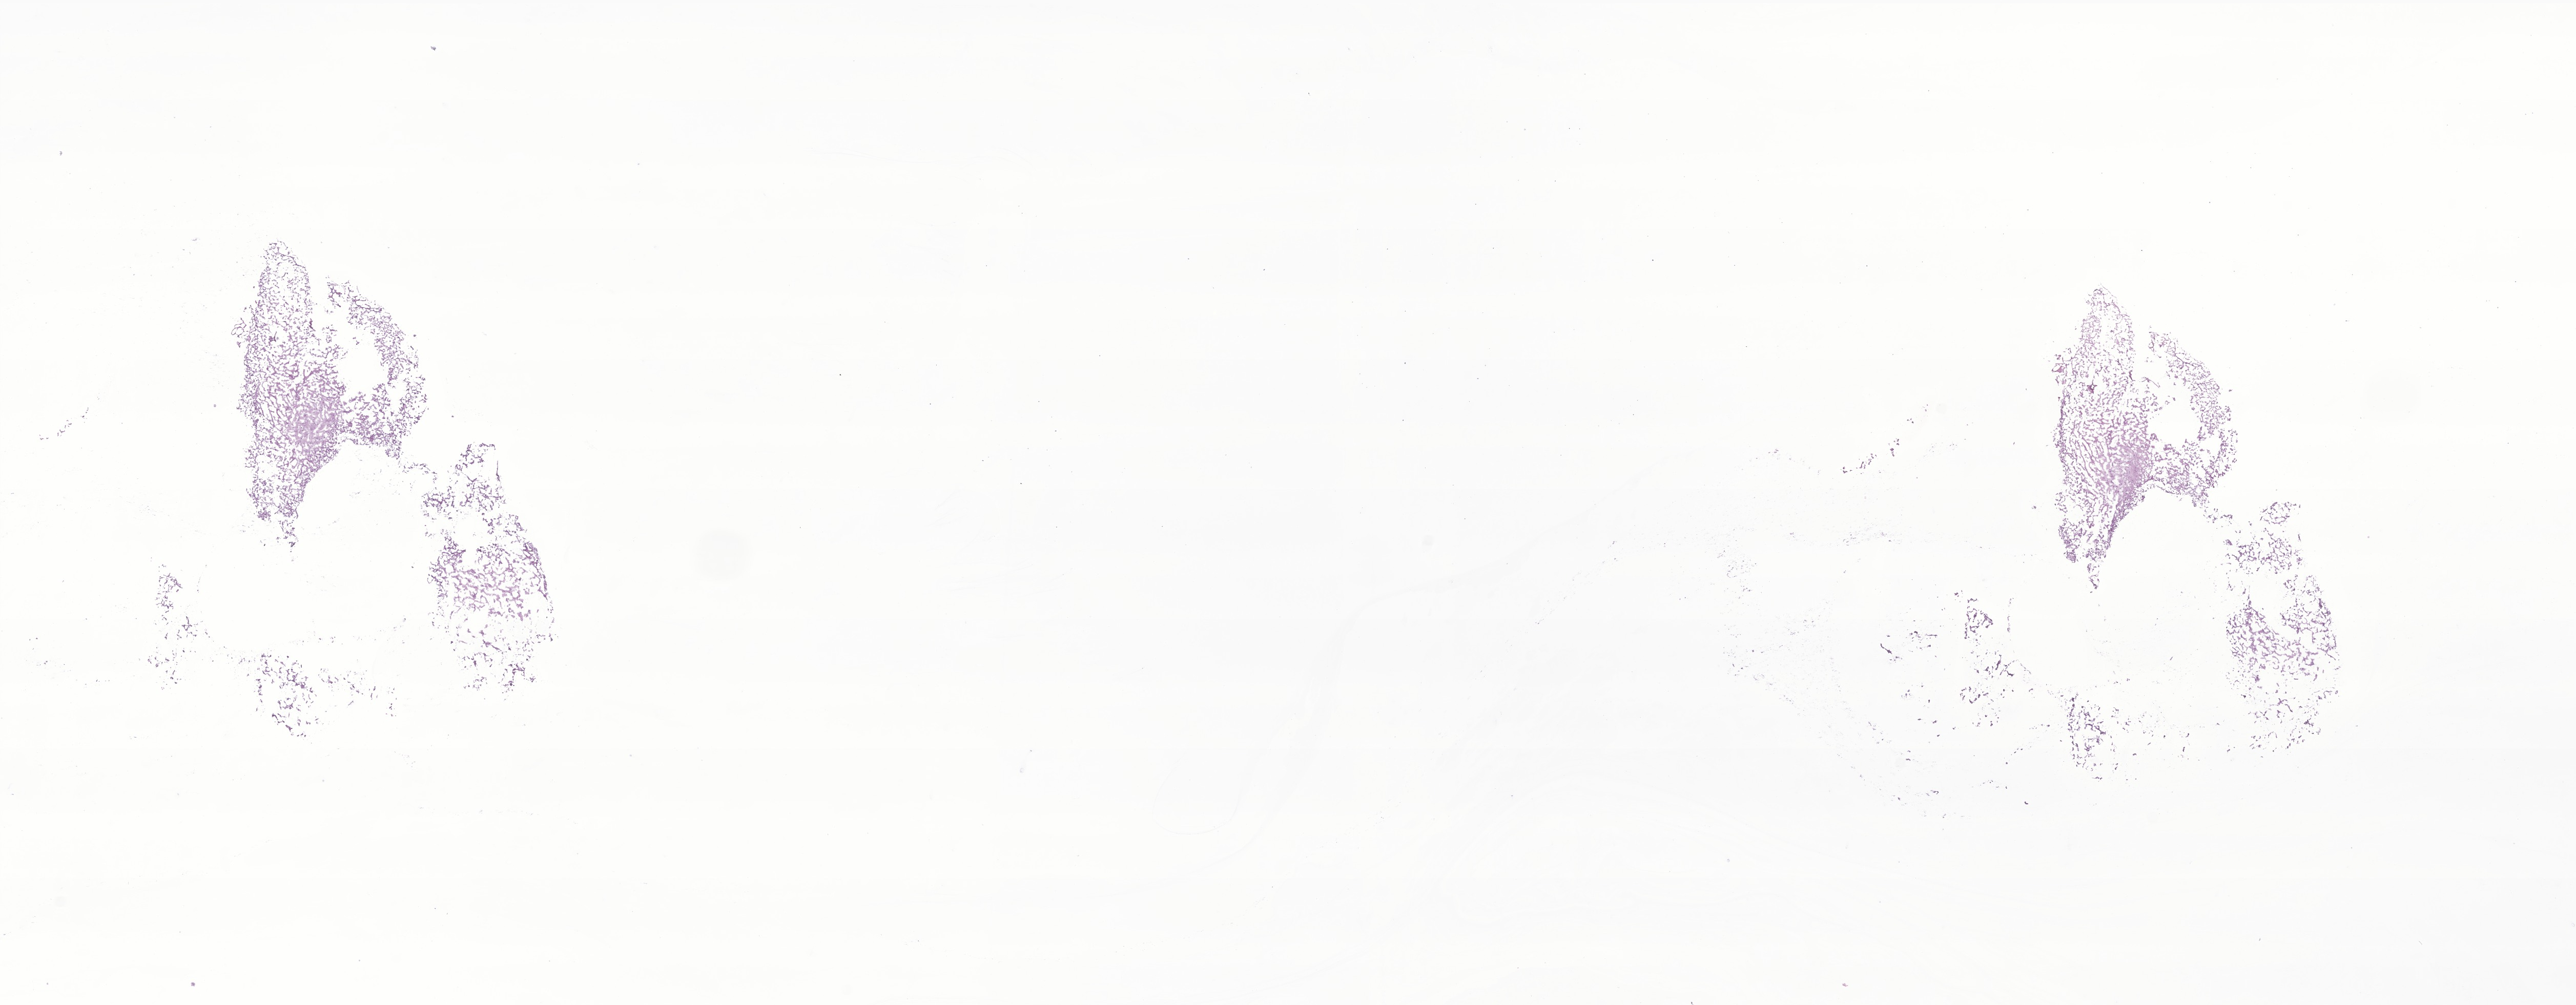
Whole-slide image, H&E stain of tumor tissue from the cerebellum, a low-resolution overview of the entire scanned area, about 21.2 x 8.3 mm. Frozen section. Patient: male, age 218 months (18 years 2 months).
* diagnosis: Pilocytic astrocytoma